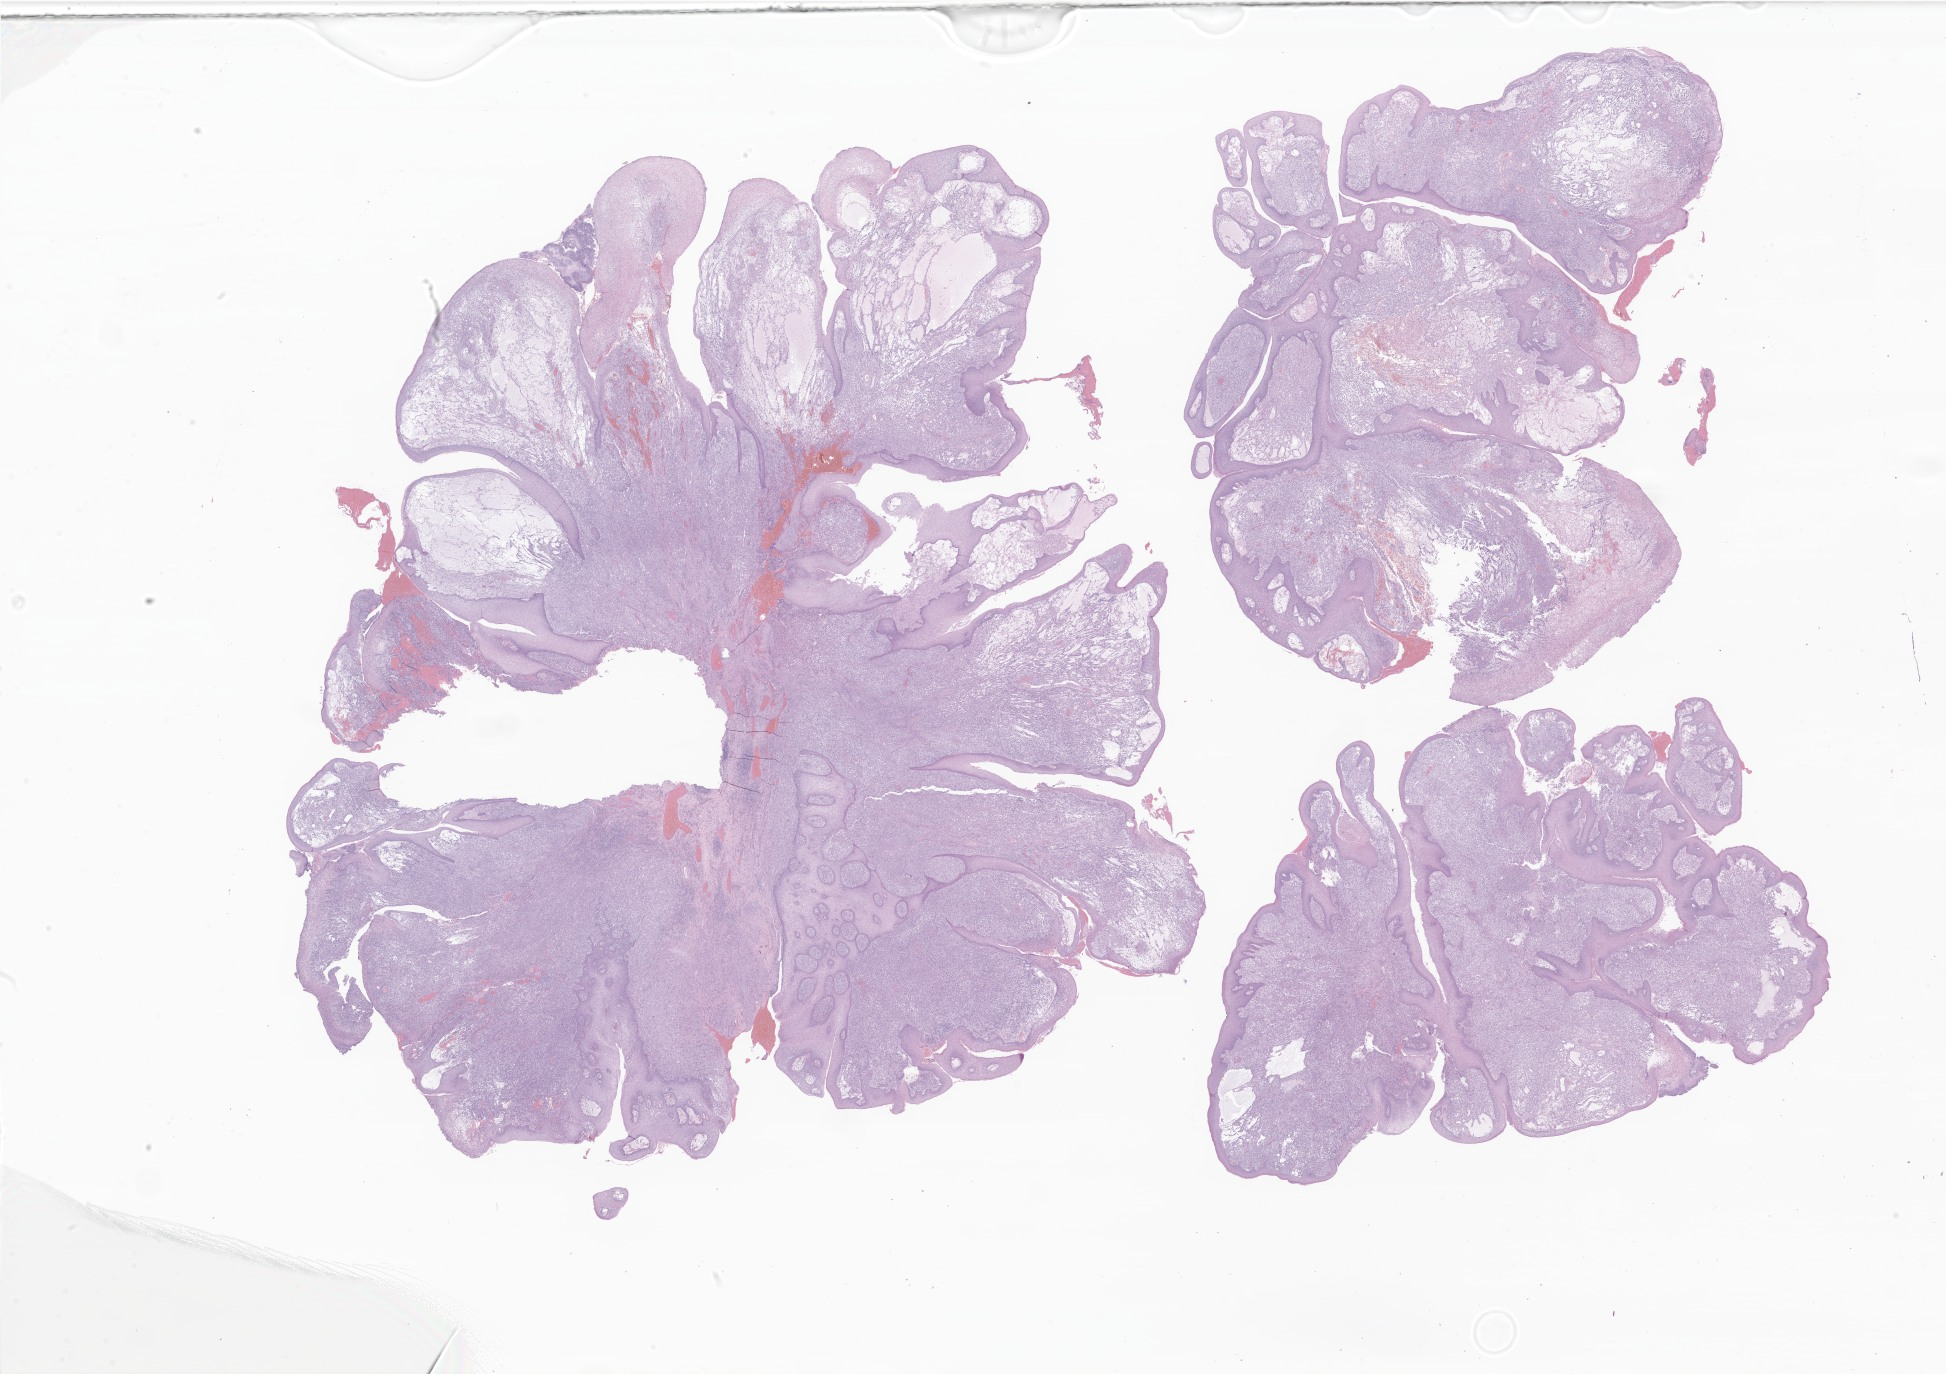
Hematoxylin and eosin (H&E) whole-slide image of tumor tissue from the oropharynx, whole scanned area (about 32.8 x 23.2 mm) shown as a low-resolution overview. Formalin-fixed paraffin-embedded section. Male patient, age 96 months (8 years).
Diagnosis (ICD-O-3 morphology term): Embryonal rhabdomyosarcoma, NOS.